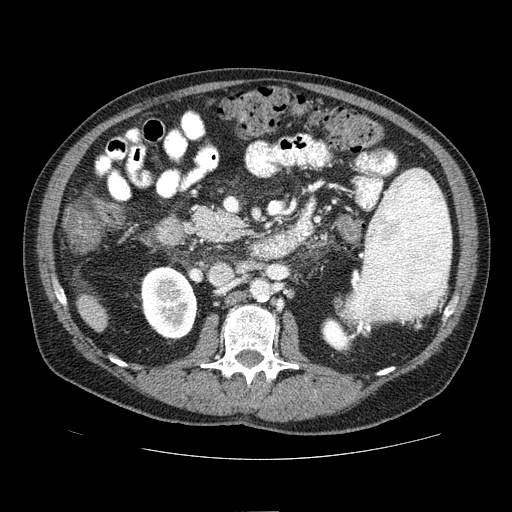
Contrast-enhanced abdominal CT (liver protocol), one axial slice. Slice 18 of 81 in the series (ordered by position). Reconstruction kernel STANDARD. 100 kVp. One of 2 acquisitions stored at this slice position. Soft-tissue window (W 400 / L 40 HU). 512 × 512 image matrix, field of view 400 × 400 mm. From the clinical record (not read from this slice): diagnosis: hepatocellular carcinoma (patient treated with transarterial chemoembolisation; whether this scan precedes or follows treatment is not stated here); TNM stage (as recorded): Stage-IIIA; Child-Pugh class: A; tumour nodularity: multinodular.
Outlined on this slice (semi-automatic segmentation, software-assisted and operator-edited):
- liver parenchyma outside the tumour (the mass and vessels are separate outlines, so this box may not span the whole liver): bounding box <78,294,106,330> (left, top, right, bottom; pixels)